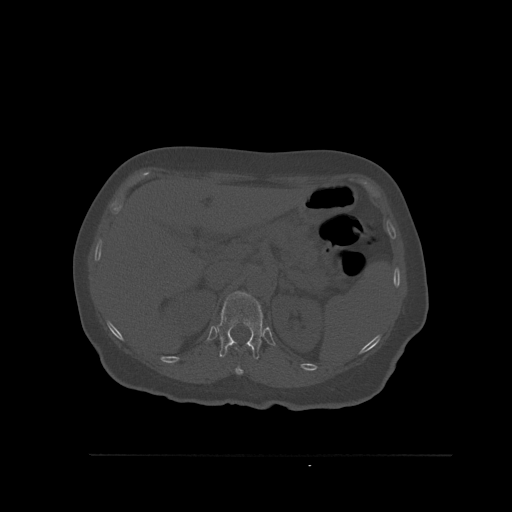
CT including the spine, one axial slice; position 288 of 527 along the scan axis; bone window (W 1800 / L 400 HU); 1.5 mm slice thickness; 512 × 512 image matrix, field of view 470 × 470 mm. Patient: female, 73 years. Case-level facts recorded for this patient, not image findings: primary cancer: breast.
Outlined on this slice (semi-automatically segmented with operator editing):
- T11 vertebra: box from (x=235, y=347) to (x=244, y=375) px
- T12 vertebra: (x=217, y=291)–(x=263, y=359)